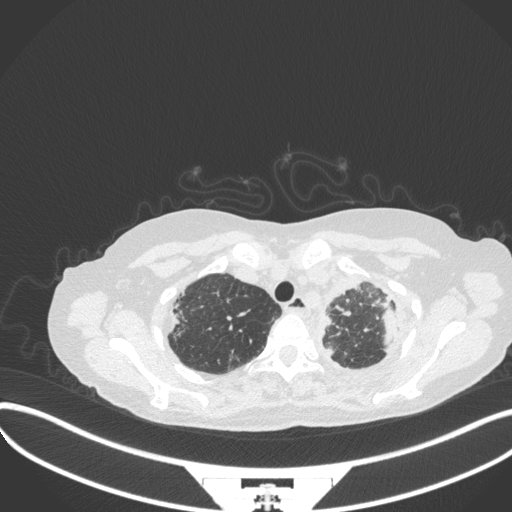
Chest CT, one axial slice. Position 290 of 373 along the scan axis. Reconstruction kernel B31f. Lung window (W 1500 / L -600 HU). 1 mm slice thickness. 512 × 512 image matrix. Patient: female, 56 years. From the clinical record (not read from this slice): clinical TNM (as recorded): T1 N0 M0.
Outlined on this slice (bounding box drawn by a radiologist):
- lung tumour (recorded histology: adenocarcinoma): box from (x=375, y=304) to (x=397, y=346) px